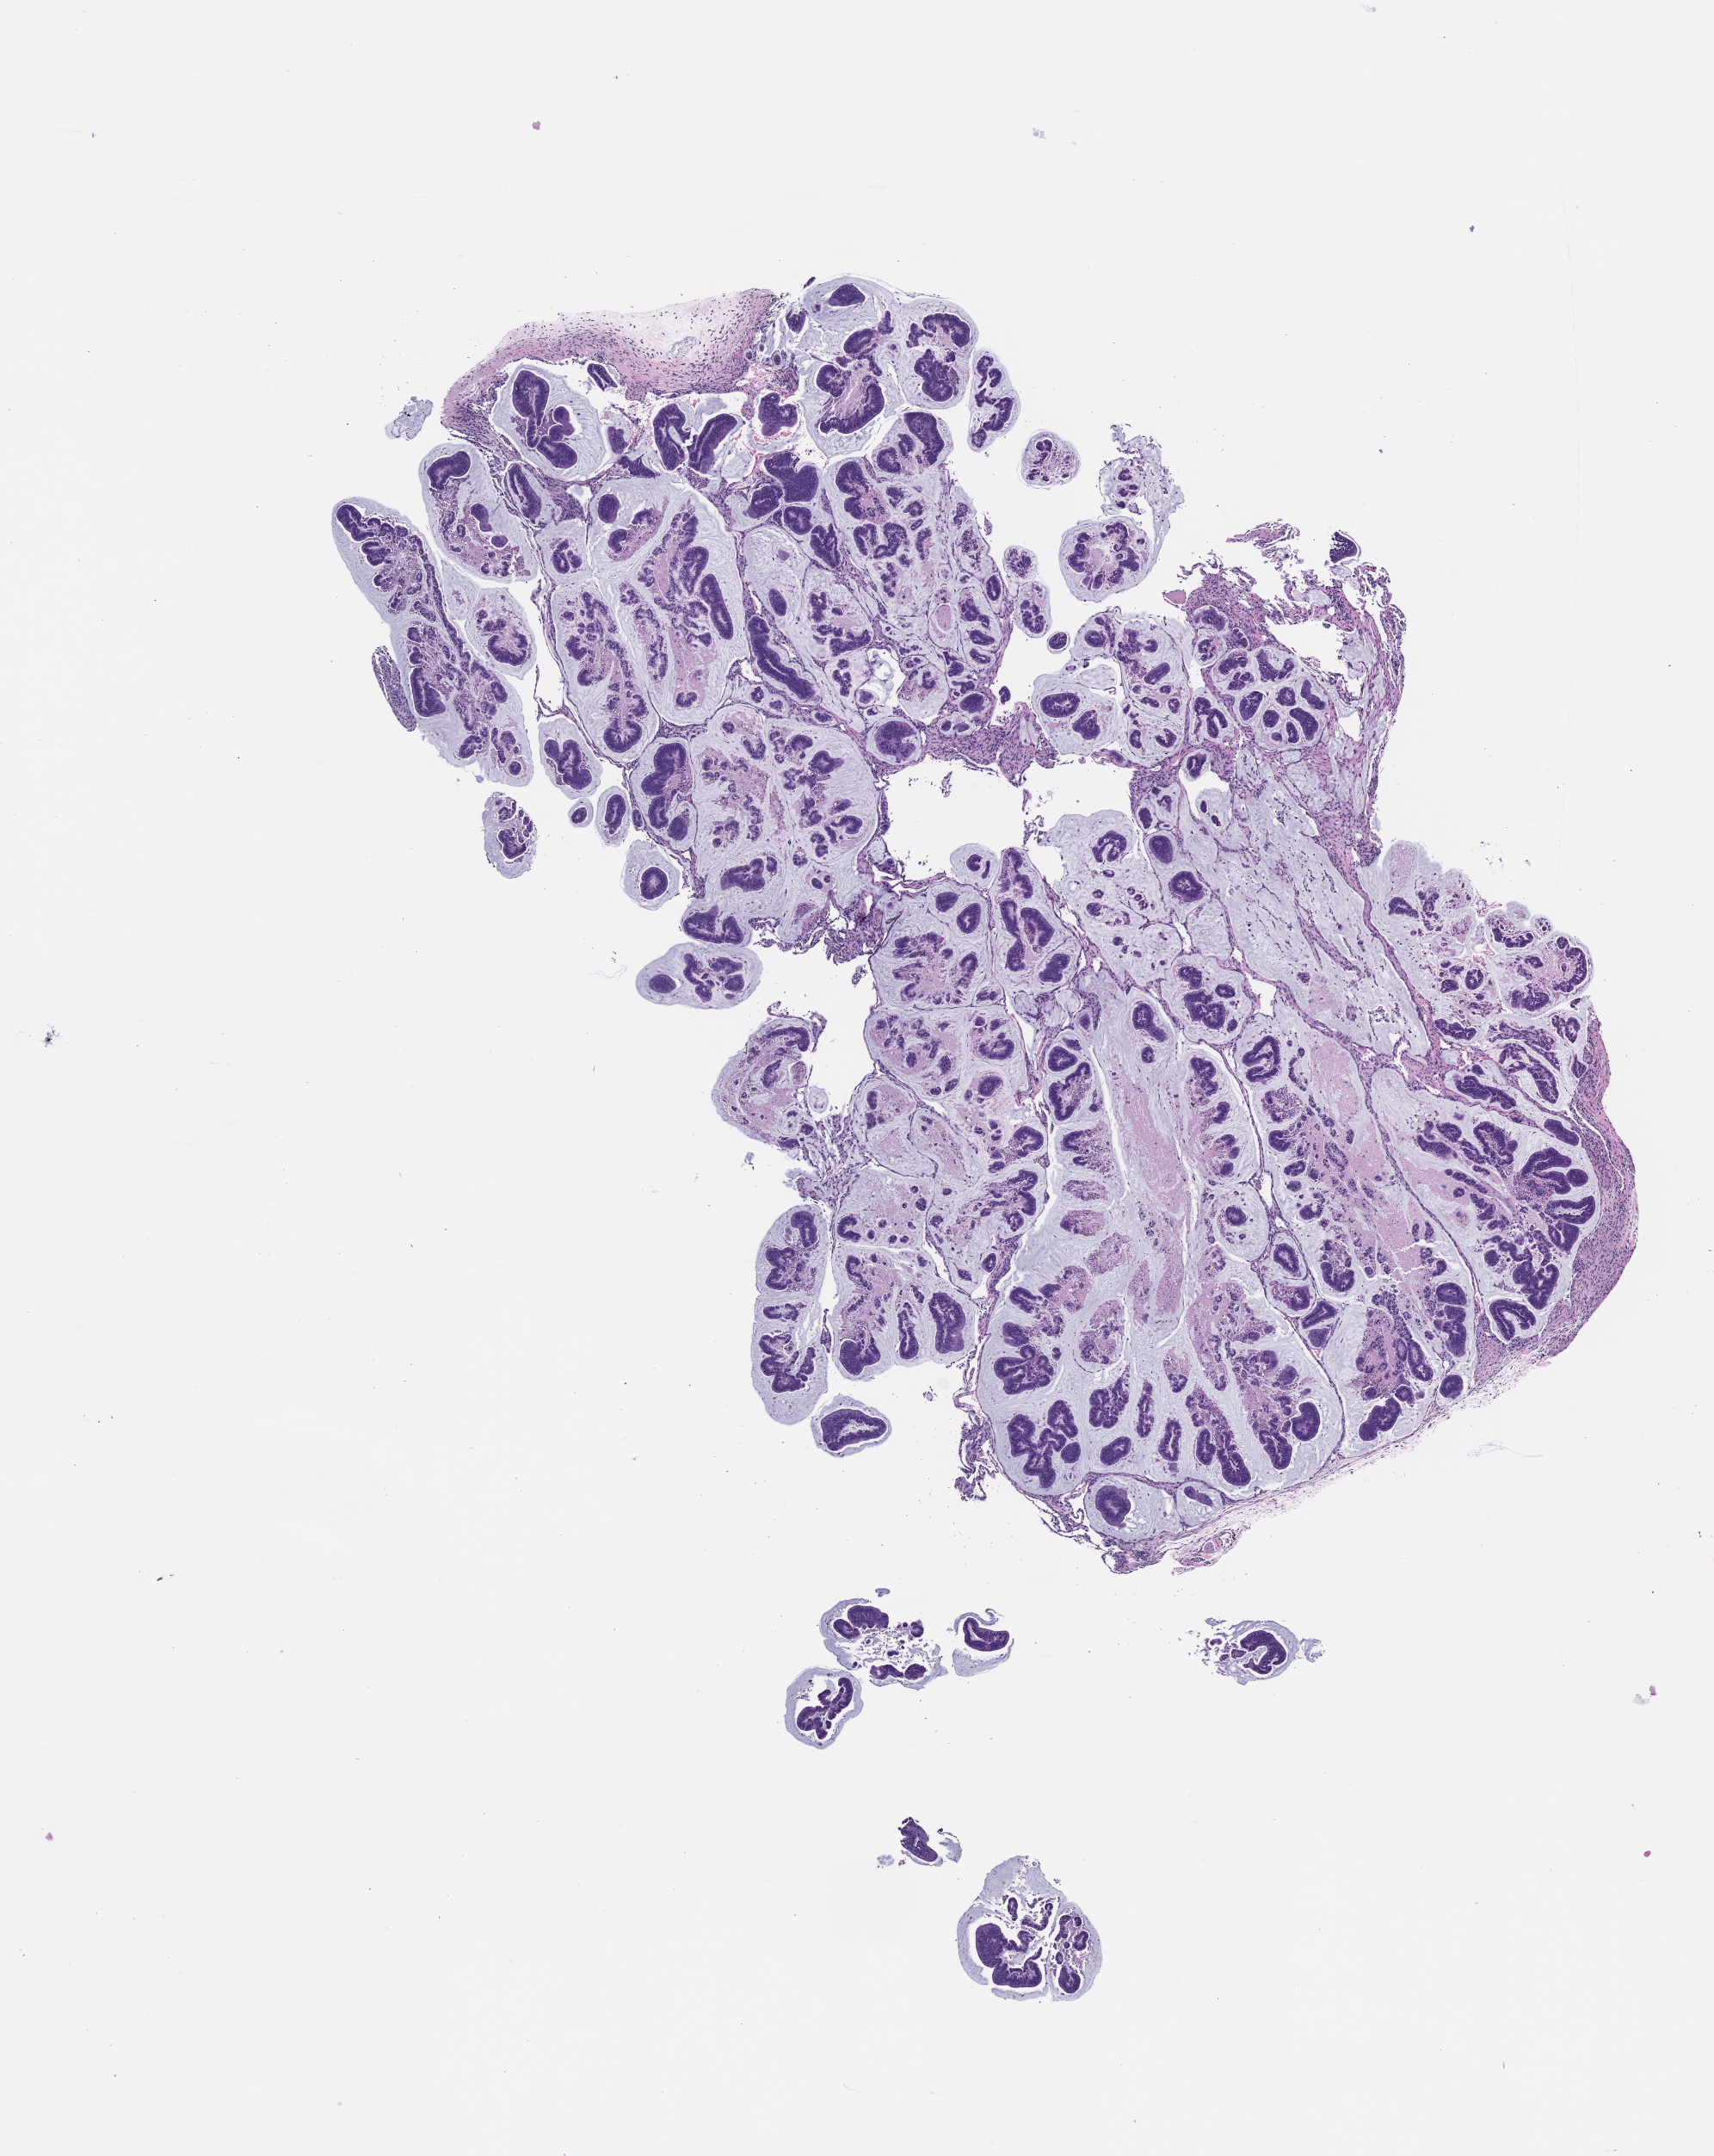
Whole-slide image, H&E: patient-derived xenograft (human tumor grown in a mouse), passage 1, whole scanned area (about 8.0 x 10.1 mm) shown as a low-resolution overview, formalin-fixed, paraffin-embedded (FFPE) tissue, tumor site category: colon.
Originating patient diagnosis: Colon Adenocarcinoma.